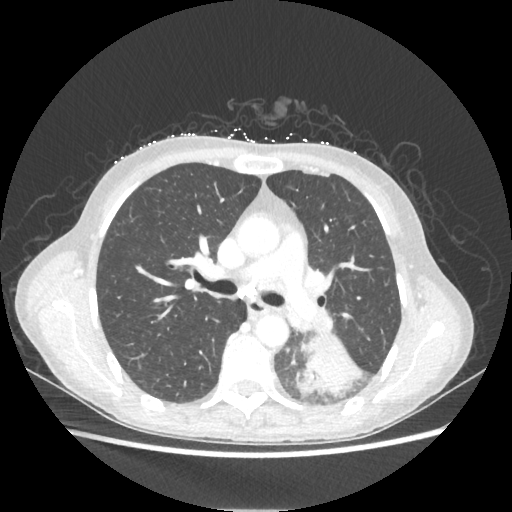
Chest CT, one axial slice. Slice 131 of 221 in the series (ordered by position). Reconstruction kernel STANDARD. Lung window (W 1500 / L -600 HU). 1.25 mm slice thickness. 512 × 512 image matrix. Female patient, age 53 years. From the clinical record (not read from this slice): clinical TNM (as recorded): T3 N0 M0.
Outlined on this slice (rectangle marked by the reading radiologist):
- lung tumour (recorded histology: adenocarcinoma): box from (x=294, y=333) to (x=362, y=397) px